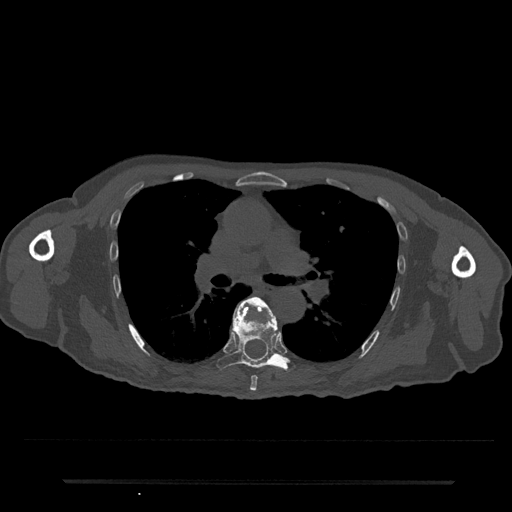
CT including the spine, one axial slice; slice 495 of 797 in the series (ordered by position); reconstruction kernel Br40s/3; 120 kVp; bone window (W 1800 / L 400 HU); 0.5 mm slice thickness; 512 × 512 image matrix, field of view 427 × 427 mm. Patient: male, 74 years. Case-level facts recorded for this patient, not image findings: primary cancer: prostate.
Structures marked on this image (semi-automatic segmentation, software-assisted and operator-edited):
- T6 vertebra: bounding box (x1, y1, x2, y2) in pixels: (235, 296, 276, 391)
- T7 vertebra: (217, 303, 295, 372)